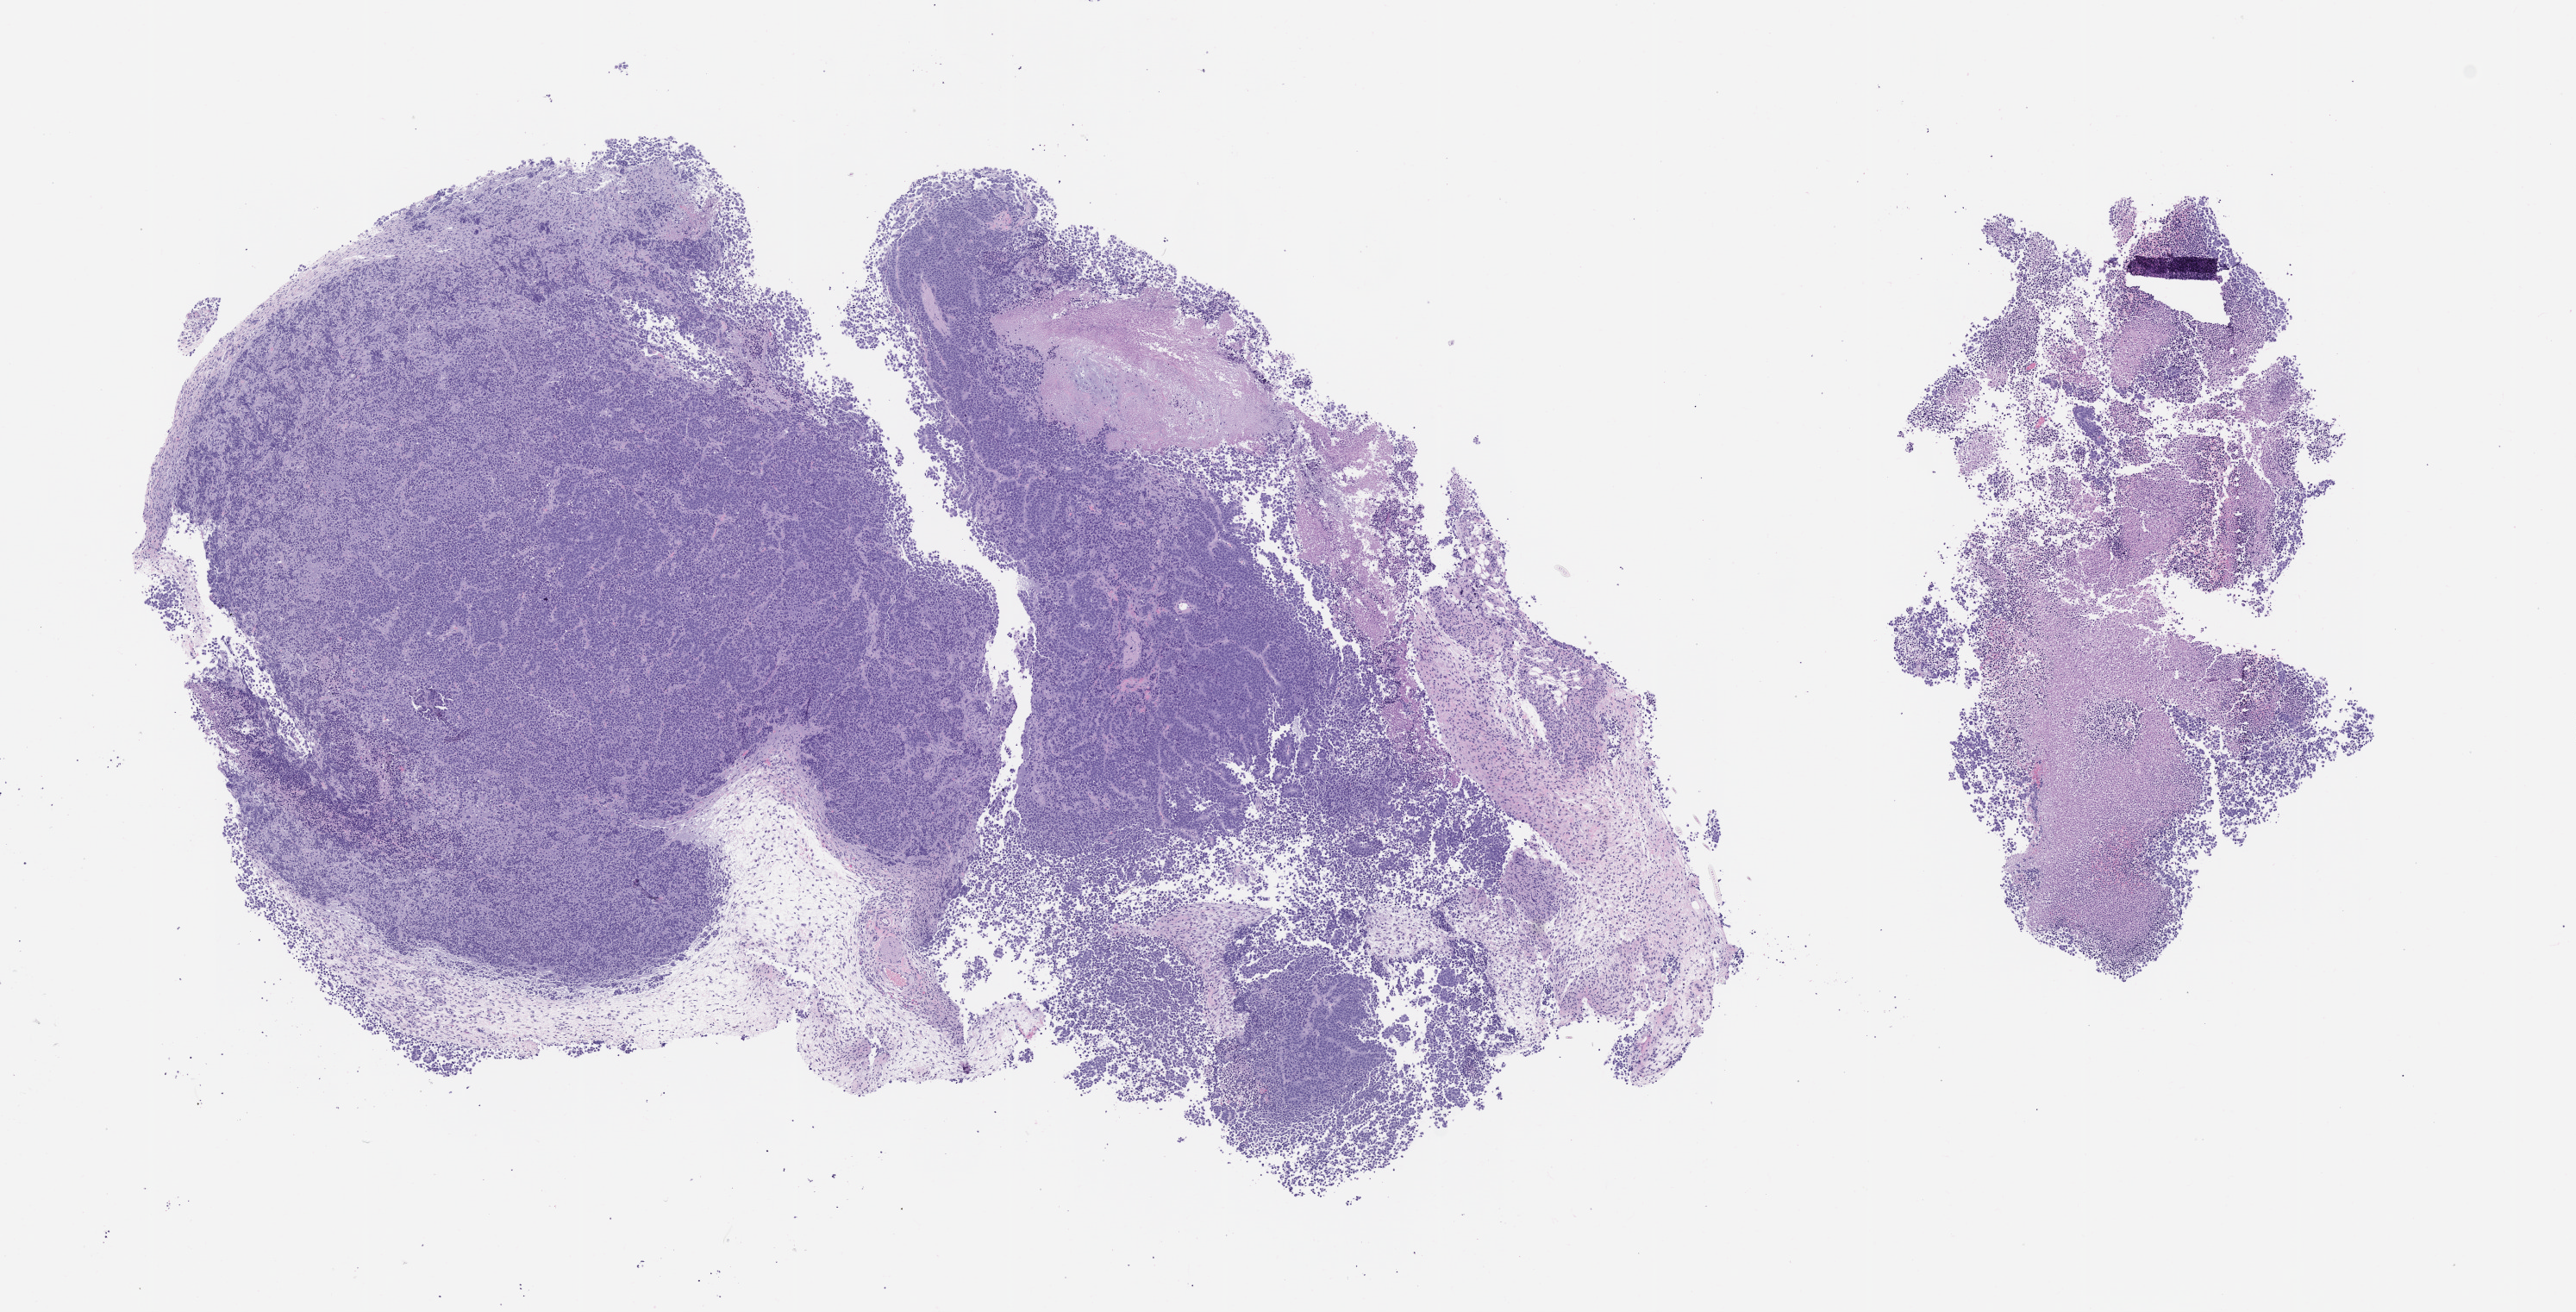
Whole-slide image, H&E: patient-derived xenograft (human tumor grown in a mouse), passage 0, shown as a low-resolution overview of the whole scanned area (about 12.0 x 6.1 mm). Formalin-fixed paraffin-embedded section. Originating tumor site category: bladder.
Originating patient diagnosis: Urothelial Carcinoma.